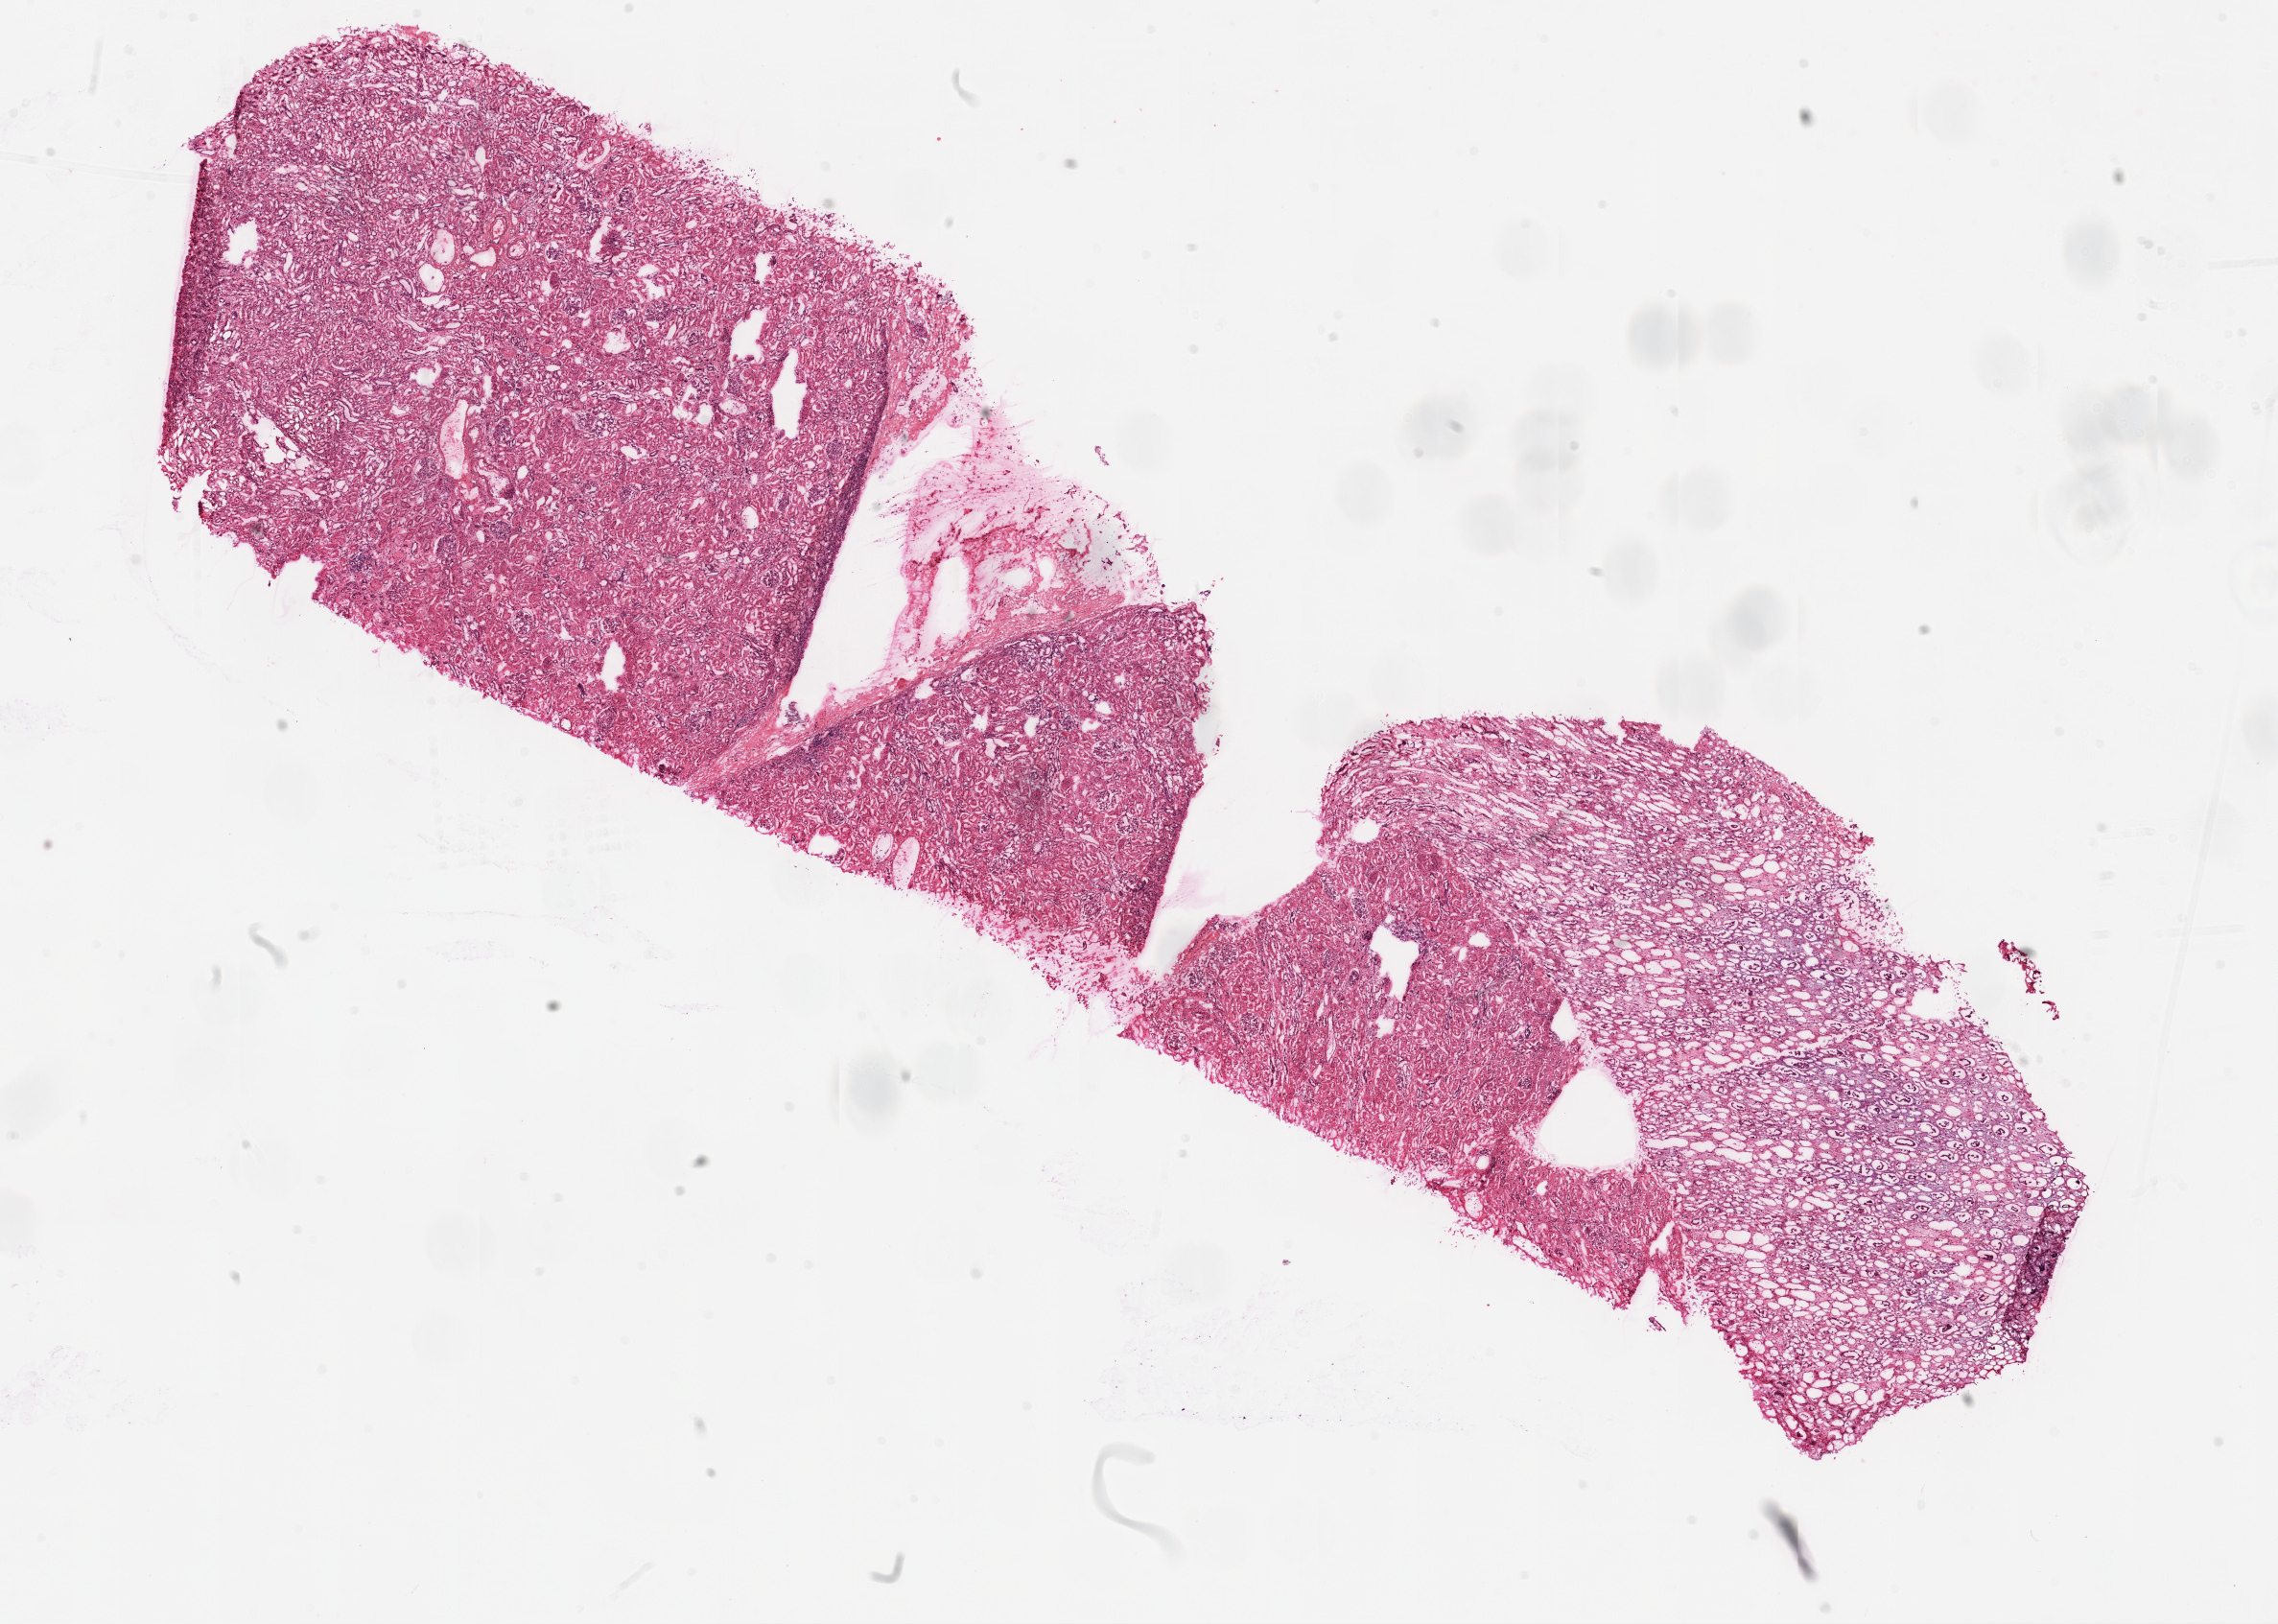
H&E-stained whole-slide image, shown as a low-resolution overview of the whole scanned area (about 19.1 x 13.6 mm); frozen section from the top of the tissue portion; kidney, solid tissue normal (non-tumour tissue) sample. Female, age 46 years at initial diagnosis.
- this section: solid tissue normal (non-tumour) sample from the same patient
- patient diagnosis: Clear cell adenocarcinoma, NOS